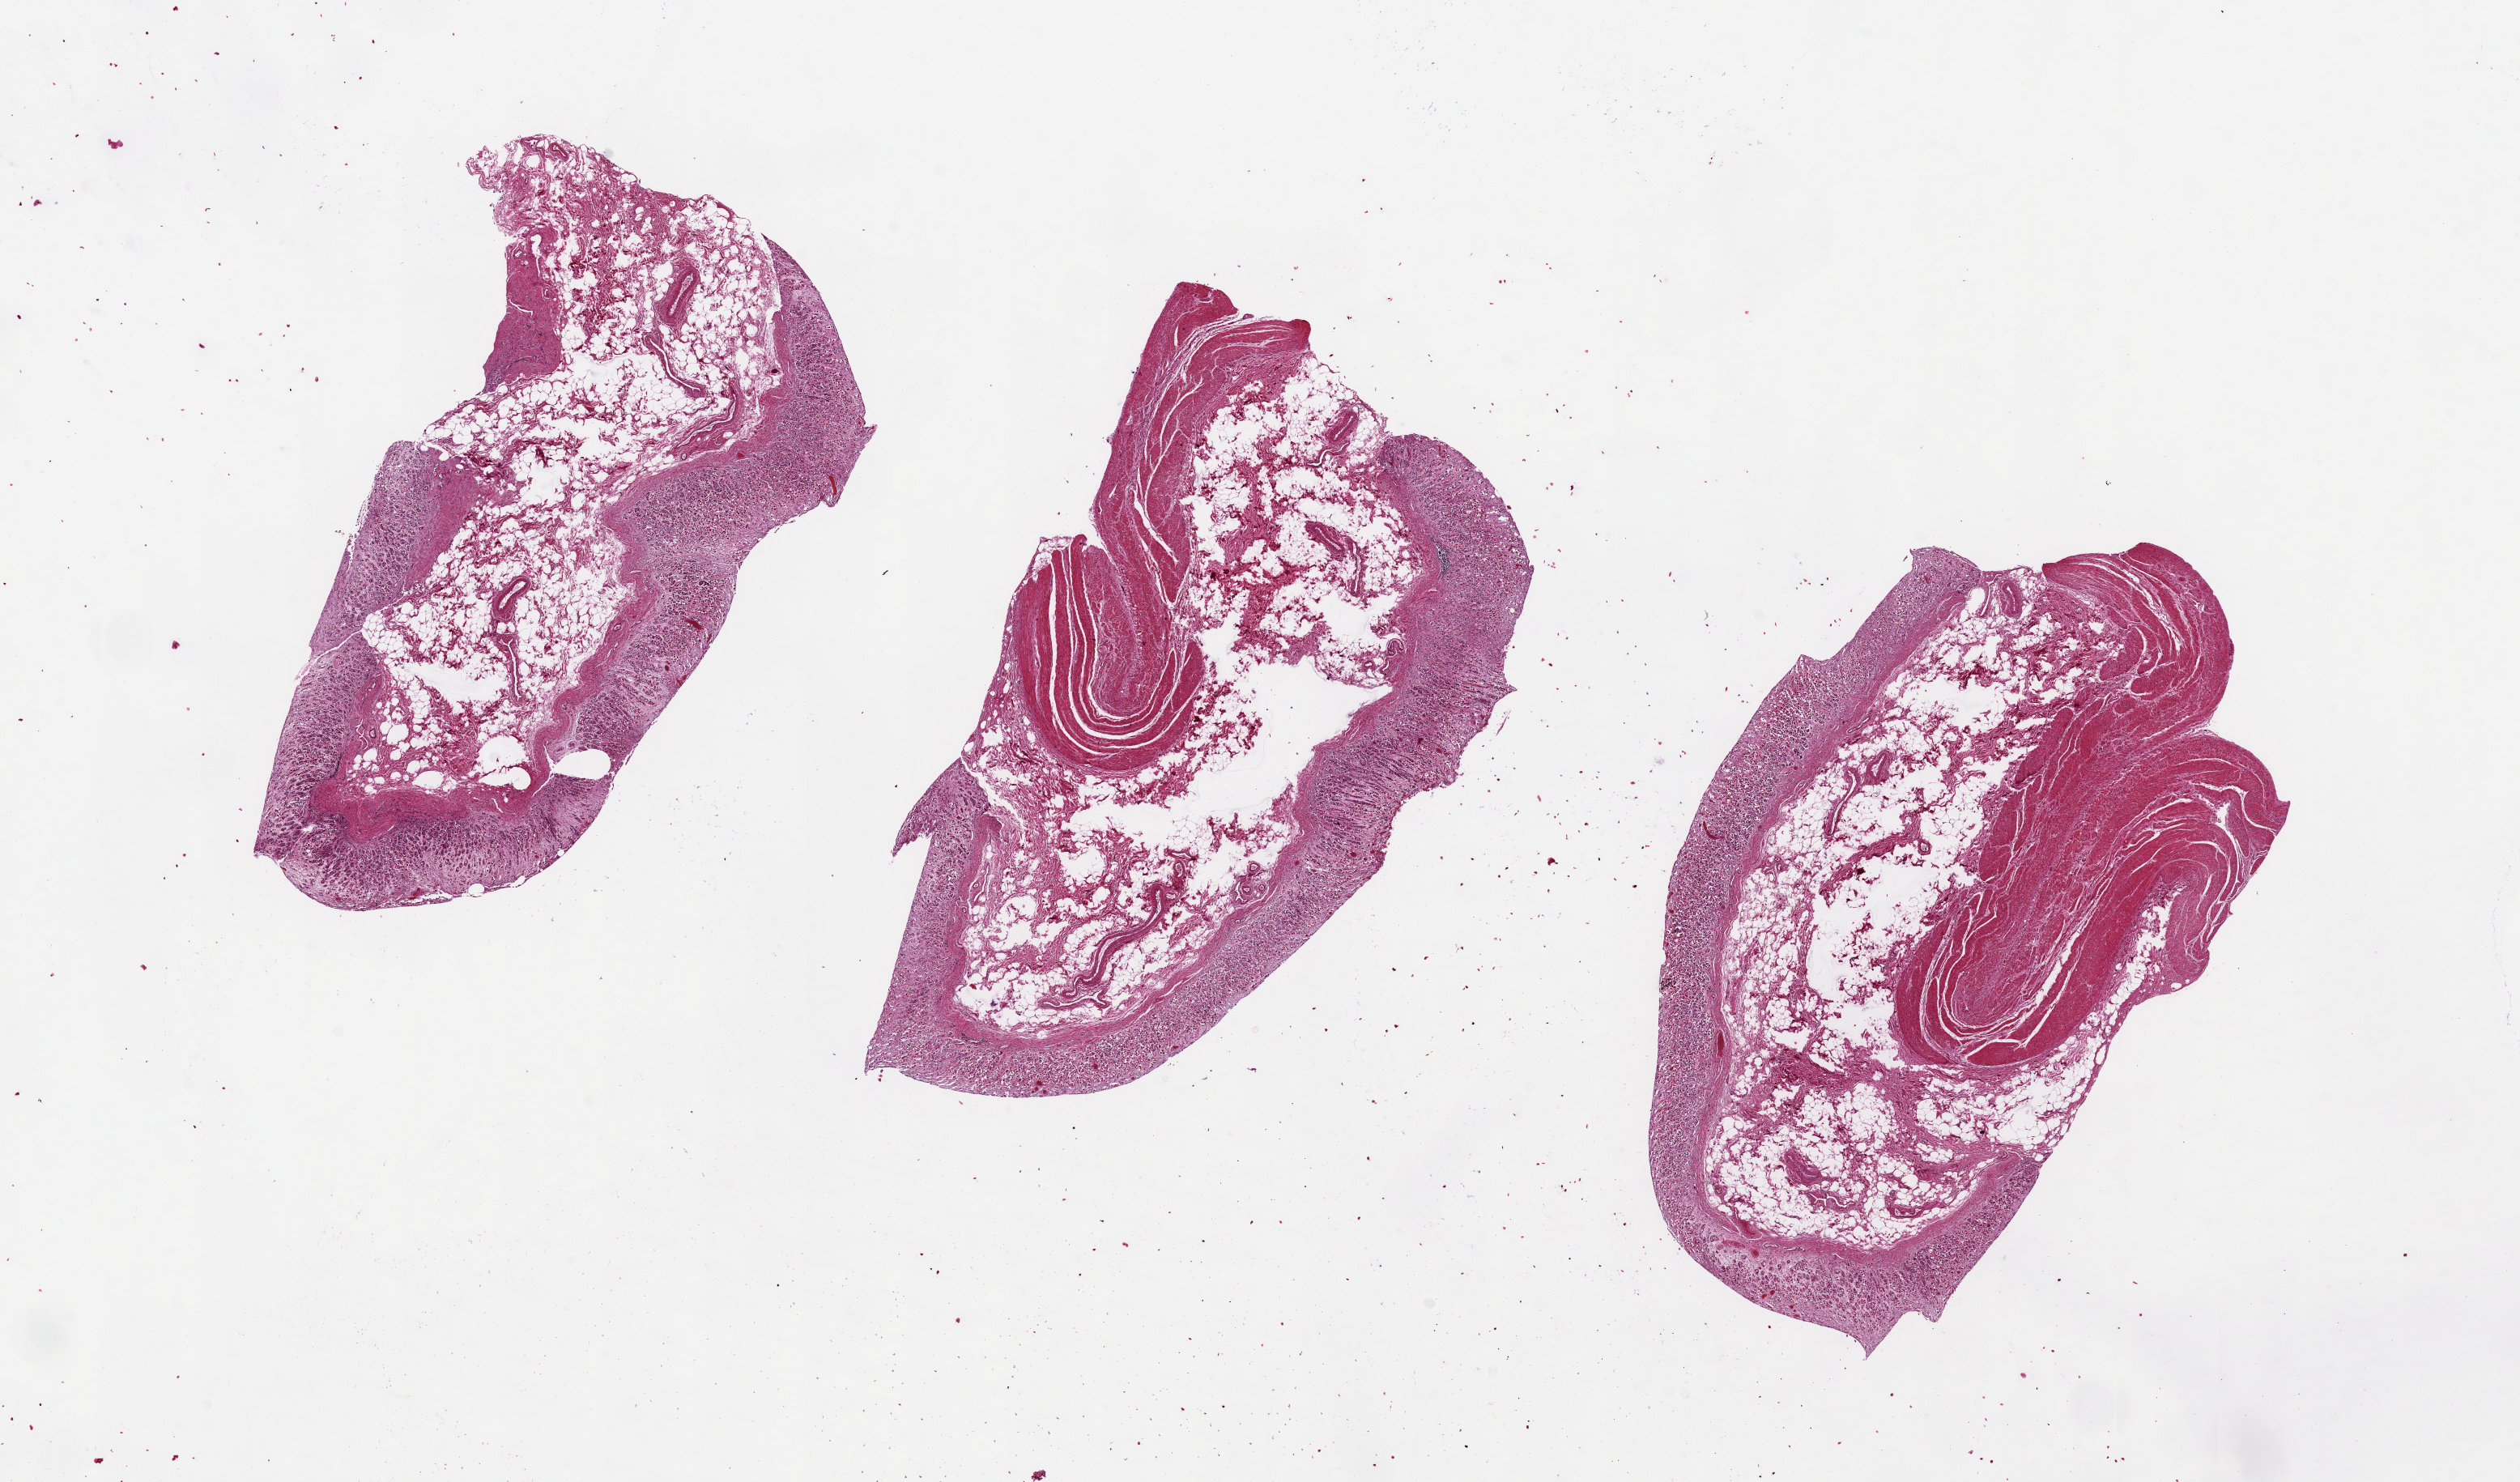
Digitized hematoxylin and eosin (H&E)-stained section, a low-resolution overview of the entire scanned area, about 24.6 x 14.5 mm (slide scanned at 20x); PAXgene-fixed, paraffin-embedded tissue; target tissue: stomach; tissue donor sample. Donor sex: male.
Reviewer comment on this tissue sample: Severely autolyzed mucosa. Moderately autolyzed muscularis.